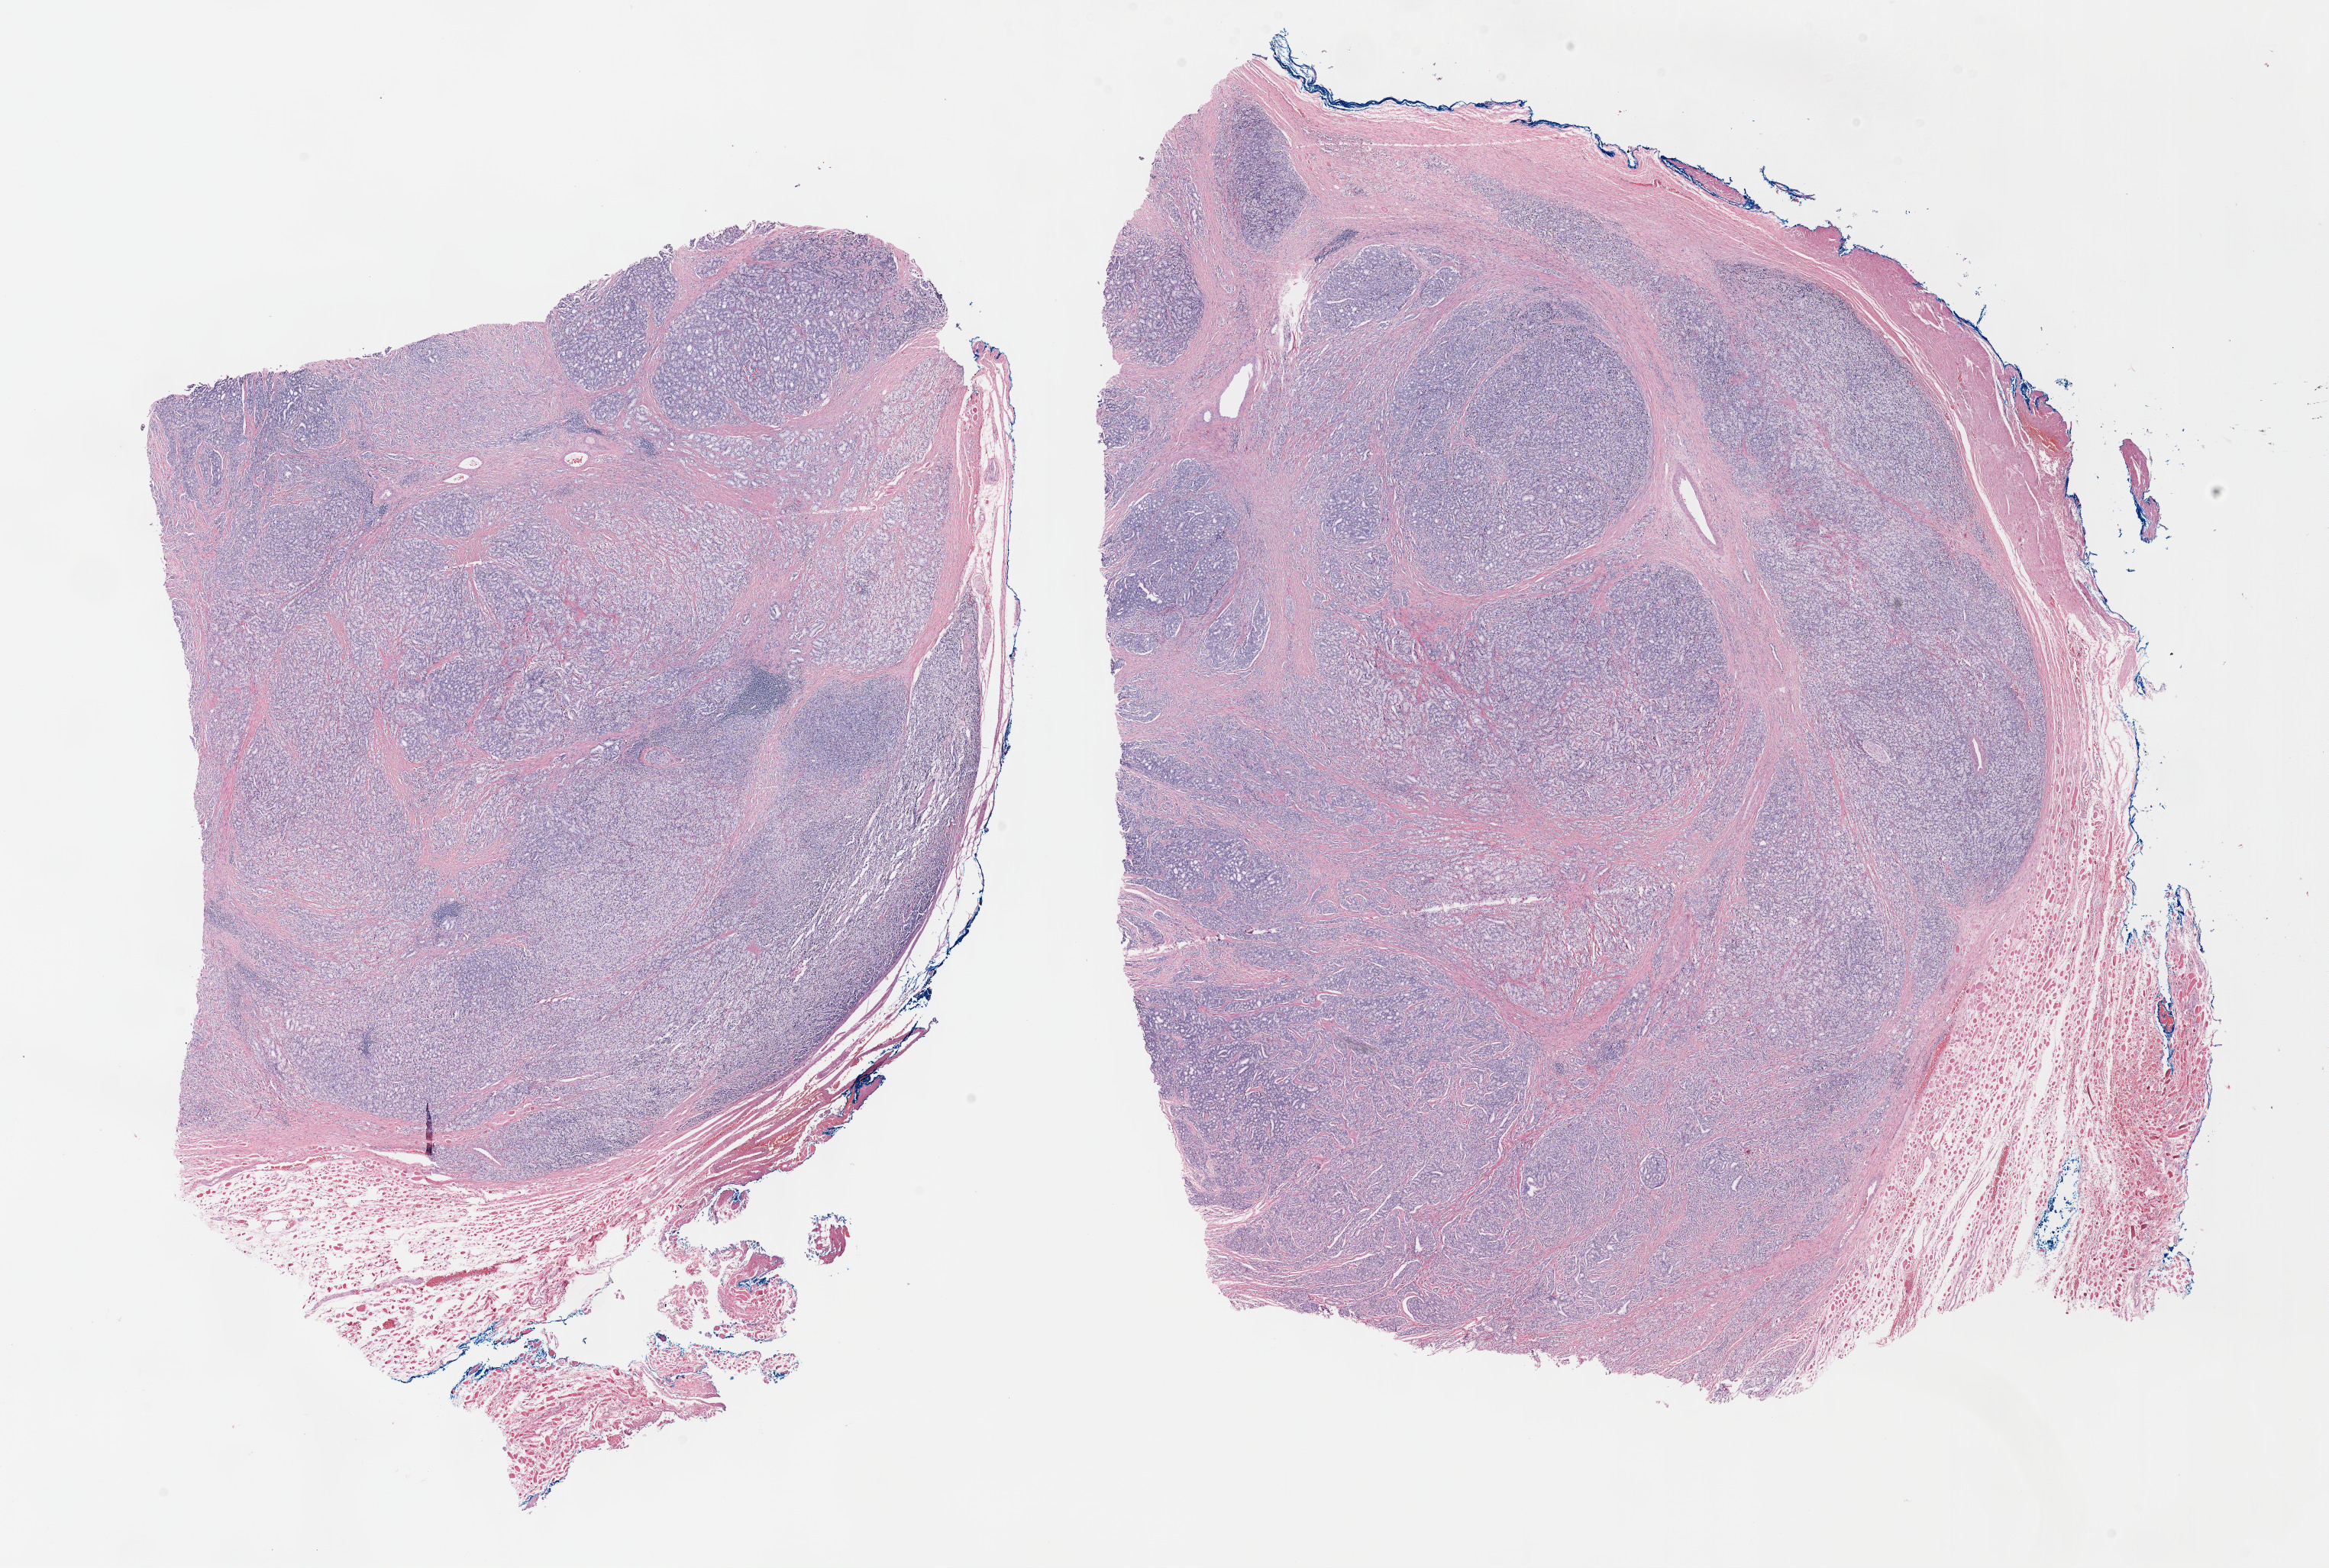
Hematoxylin and eosin (H&E) stained whole-slide image — shown as a low-resolution overview of the whole scanned area (about 24.7 x 16.6 mm, acquisition: 40x scan); formalin-fixed paraffin-embedded (FFPE) diagnostic section; prostate, primary tumour sample. Male patient; age at initial diagnosis 70 years. Gleason score: 8 (4+4).
* histologic diagnosis: Adenocarcinoma, NOS (prostate gland)
* lymph nodes positive (case pathology): 0 of 4 examined